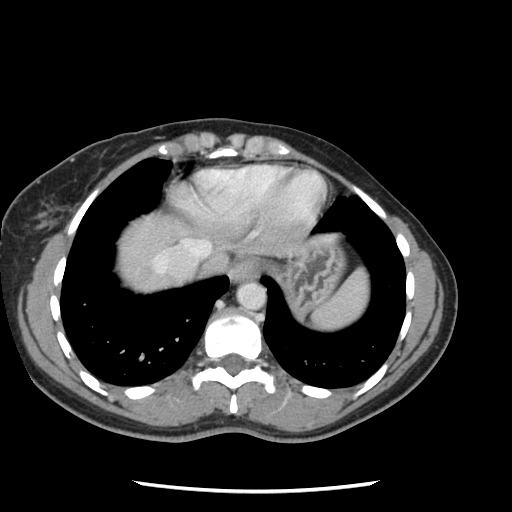
Contrast-enhanced abdominal CT, one axial slice. Slice 111 of 134 in the series (ordered by position). 120 kVp. Intravenous contrast given. Soft-tissue window (W 400 / L 40 HU). 2.5 mm slice thickness. 512 × 512 image matrix. Female patient, age 43 years. Case-level facts recorded for this patient, not image findings: diagnosis: colorectal cancer liver metastases, imaged before liver resection; multiple liver metastases: yes; largest metastasis: 3.4 cm.
Outlined on this slice (expert manual segmentation):
- hepatic veins: bounding box (x1, y1, x2, y2) in pixels: (155, 239, 210, 272)
- liver: (121, 213, 185, 290)
- planned liver remnant (the part of the liver to remain after resection): (121, 214, 186, 284)